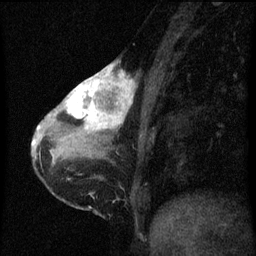
Breast MRI (dynamic contrast-enhanced), one sagittal slice; dynamic contrast-enhanced series, image 2 of 3 at this slice position (ordered by acquisition); 1.5 T; TE 4.2 ms, TR 8 ms; 2 mm slice thickness; 256 × 256 image matrix, field of view 180 × 180 mm. Patient: female, 38 years.
Structures marked on this image (semi-automatic segmentation, software-assisted and operator-edited):
- analysis volume of interest (the breast-tissue region the enhancement analysis was run in; not a lesion): box from (x=61, y=64) to (x=135, y=147) px
- tumour enhancement mask (voxels above the 70 % enhancement threshold inside the analysis volume of interest): (x=64, y=64)–(x=134, y=131)